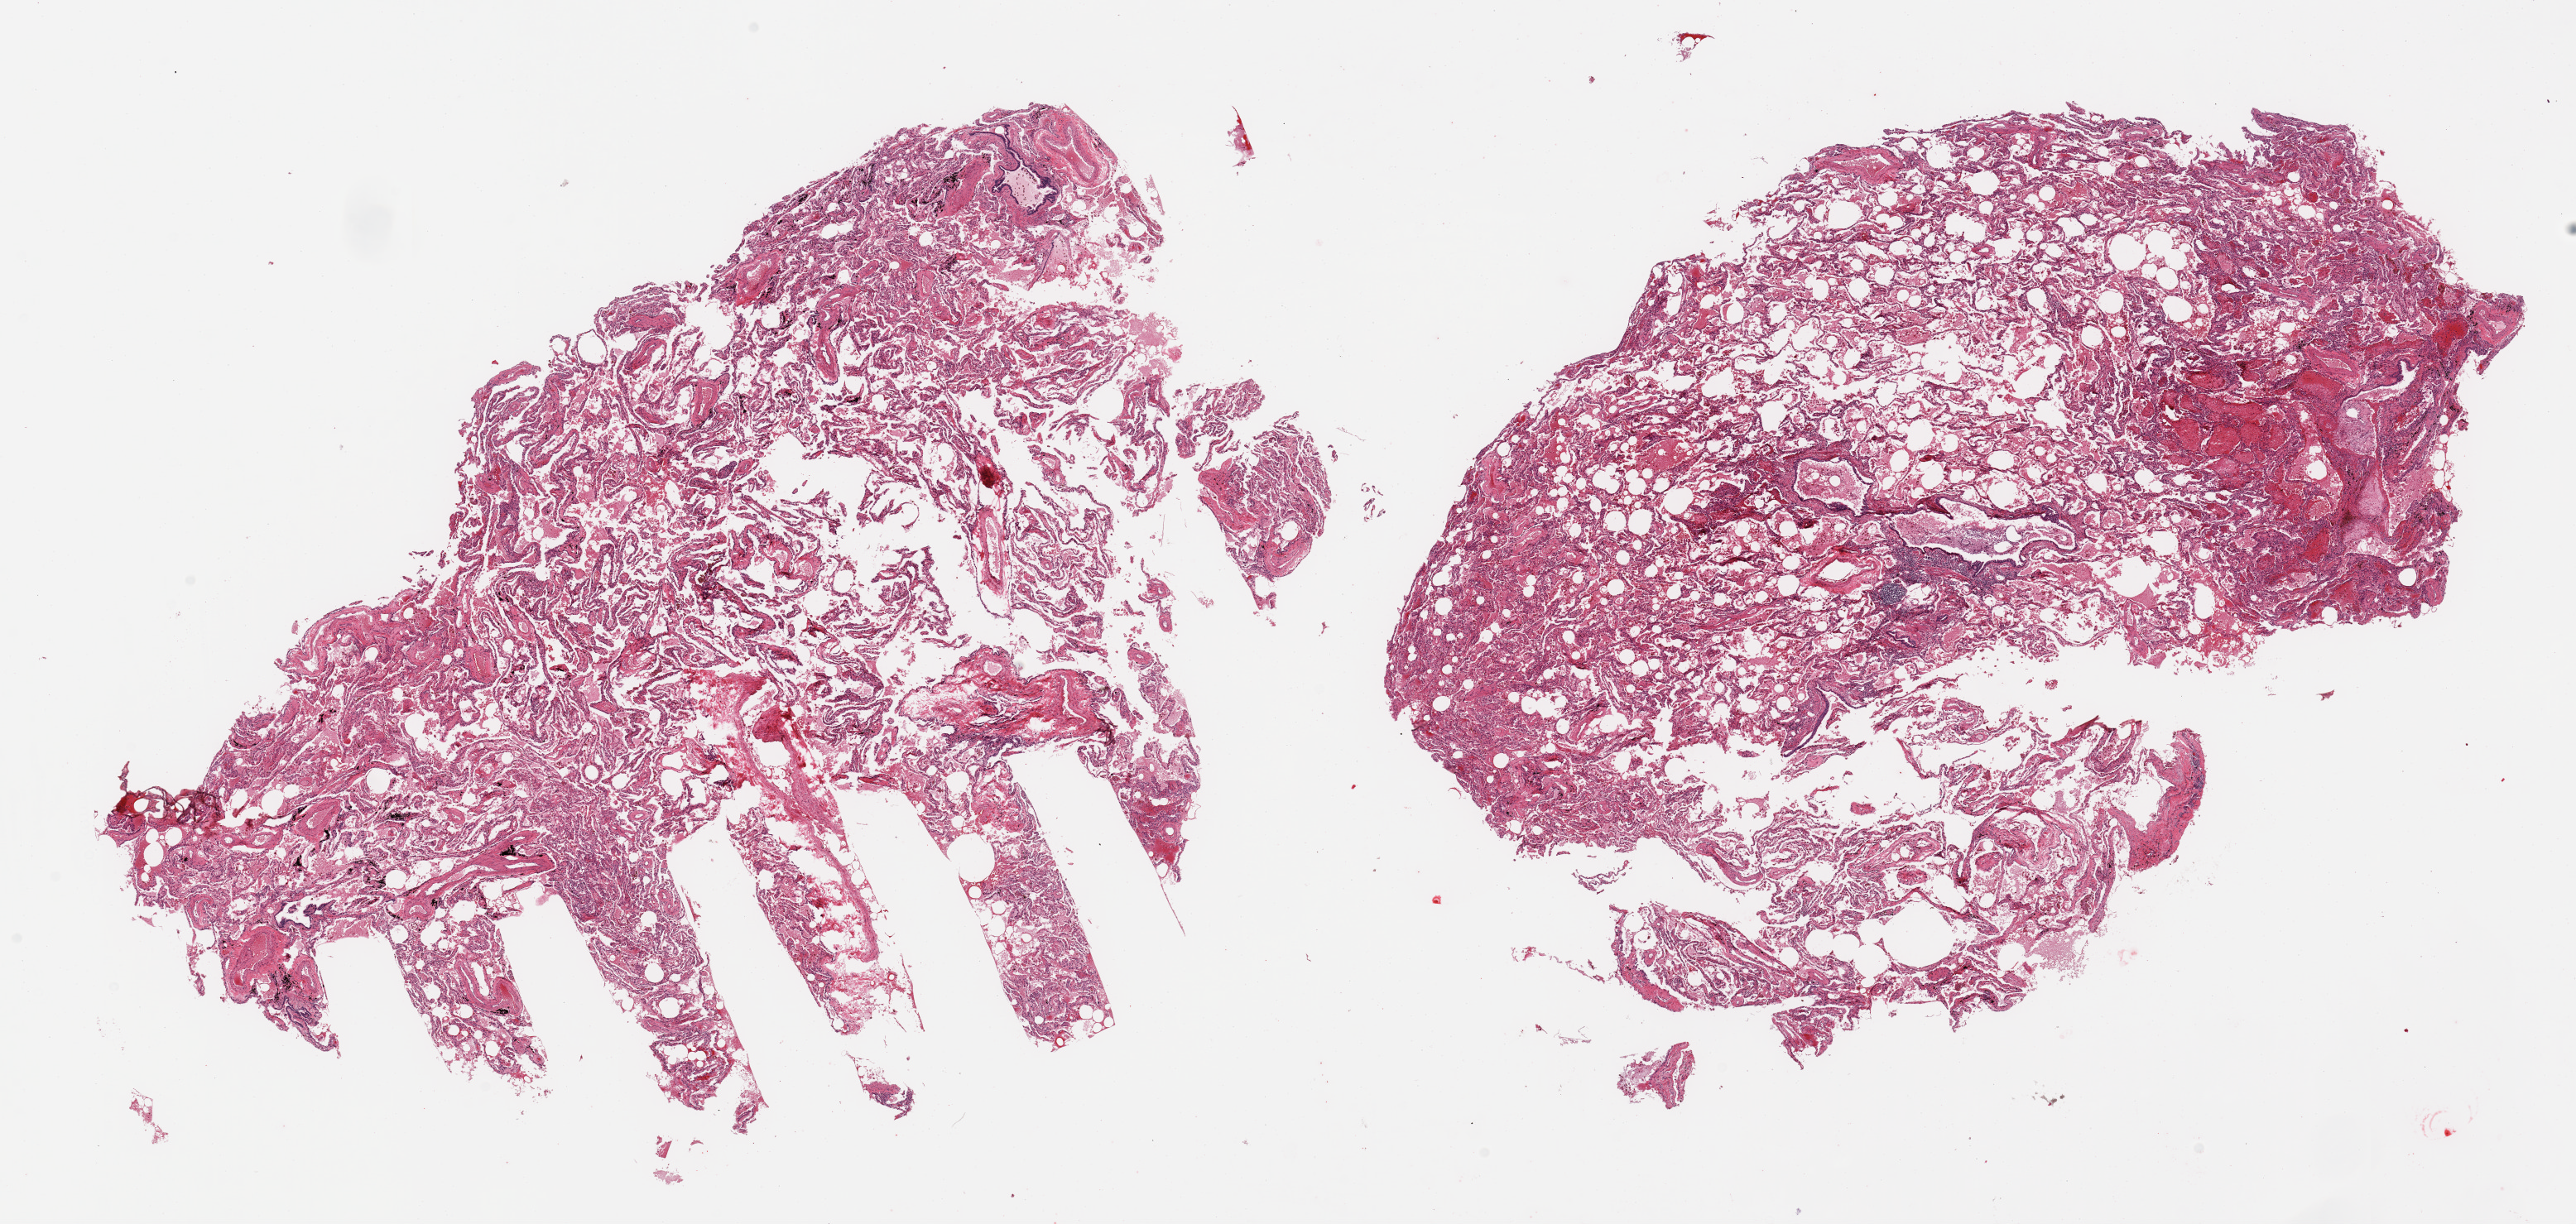
Digitized hematoxylin and eosin (H&E)-stained section — a low-resolution overview of the entire scanned area, about 24.6 x 11.7 mm, PAXgene-fixed paraffin-embedded (PFPE) section, sampled site (target tissue): lung, tissue donor sample. Male donor.
Pathologist's review note for this sample: 2 pieces patchy chronic, focally acute pneumonitis.